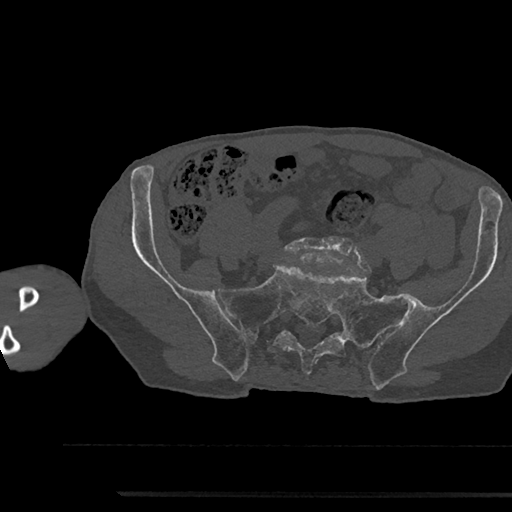
CT including the spine, one axial slice; reconstruction kernel Br40s/3; 120 kVp; bone window (W 1800 / L 400 HU); 0.5 mm slice thickness; 512 × 512 image matrix, field of view 367 × 367 mm. Male patient, age 79 years. From the clinical record (not read from this slice): primary cancer: prostate.
Structures marked on this image (semi-automatic segmentation, software-assisted and operator-edited):
- L5 vertebra: bounding box [x1, y1, x2, y2] px = [284, 238, 367, 268]